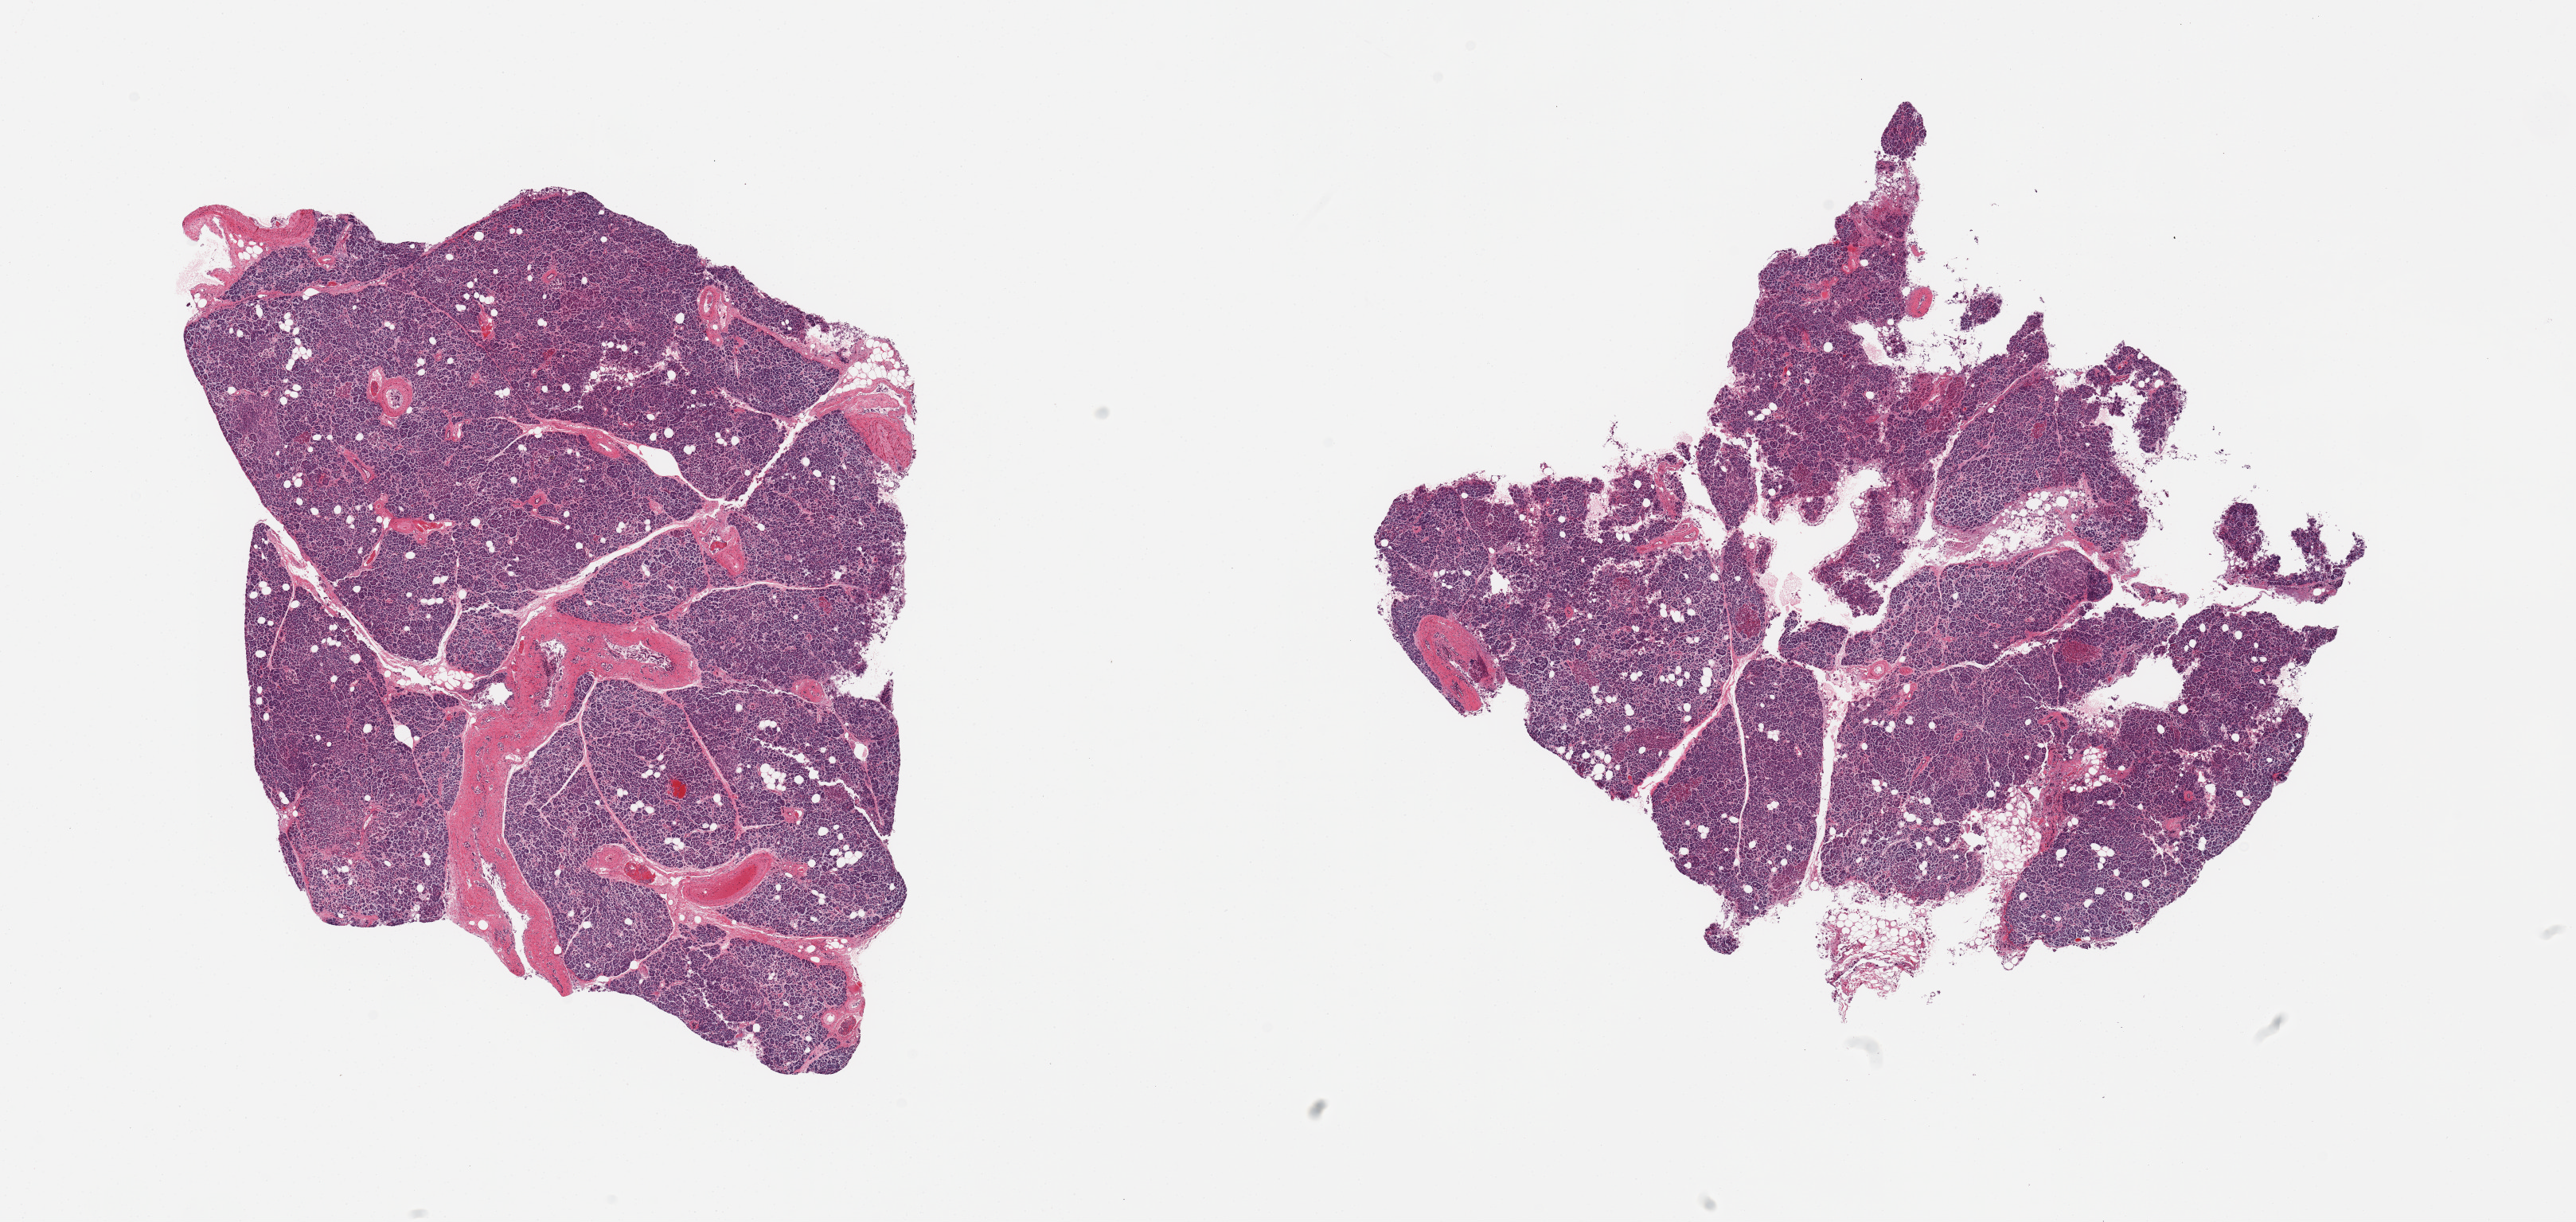
Whole-slide image, hematoxylin and eosin (H&E) stain, brightfield — a low-resolution overview of the entire scanned area, about 25.6 x 12.1 mm (slide scanned at 20x). PAXgene-fixed, paraffin-embedded tissue. Target tissue: pancreas. Tissue donor sample. Donor: male.
Pathologist's review note for this sample: 2 pieces score 2 approaching 3....moderate-focally marked autolysis/saponification; Rare Islets noted (1), but generally poorly seen.